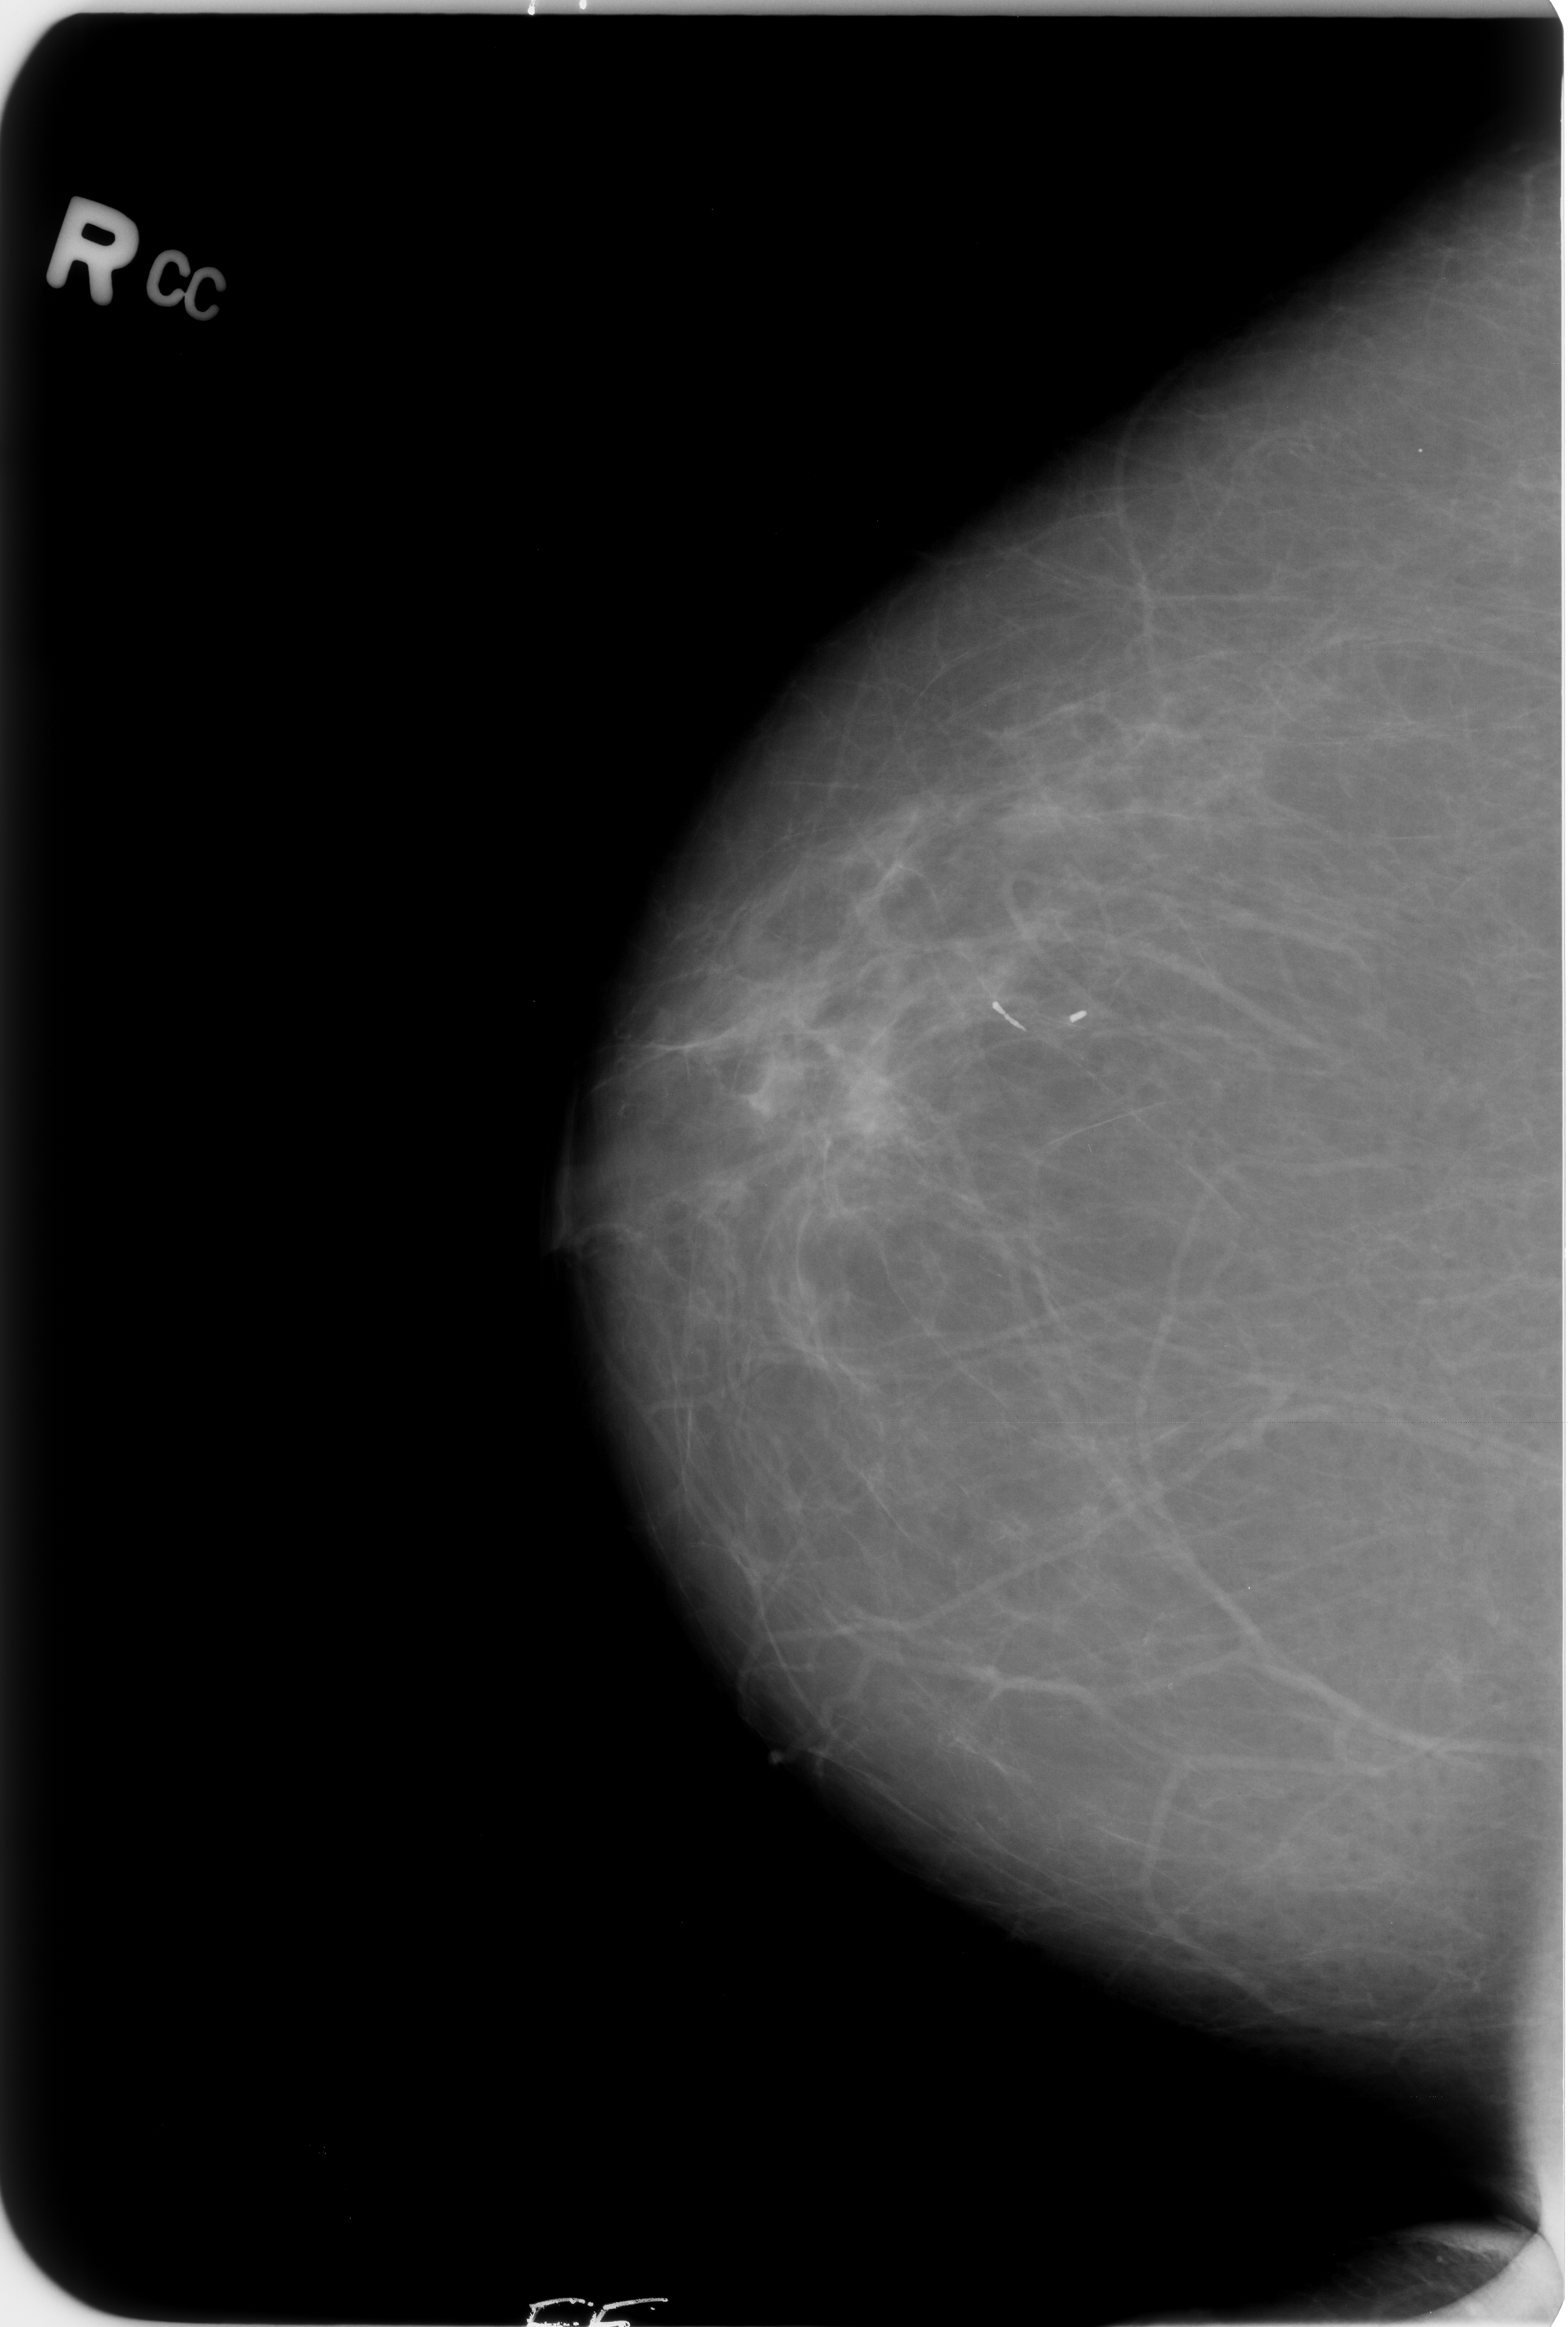
Scanned film-screen mammogram. Right breast. CC view. Breast composition: almost entirely fatty (BI-RADS density category 1 of 4). 1568 × 2327 image matrix.
Expert-marked regions of interest on this film, with their recorded descriptors:
- Finding 1 of 2: calcifications, morphology large rodlike, distribution segmental; BI-RADS assessment category 2; outcome (as recorded, no biopsy): benign without callback (not worked up further): bounding box [x1, y1, x2, y2] px = [976, 982, 1038, 1060]
- Finding 2 of 2: calcifications, morphology large rodlike, distribution segmental; BI-RADS assessment category 2; subtlety rating 5 on a 1 (subtle) to 5 (obvious) scale; outcome (as recorded, no biopsy): benign without callback (not worked up further): [1046, 992, 1114, 1051]